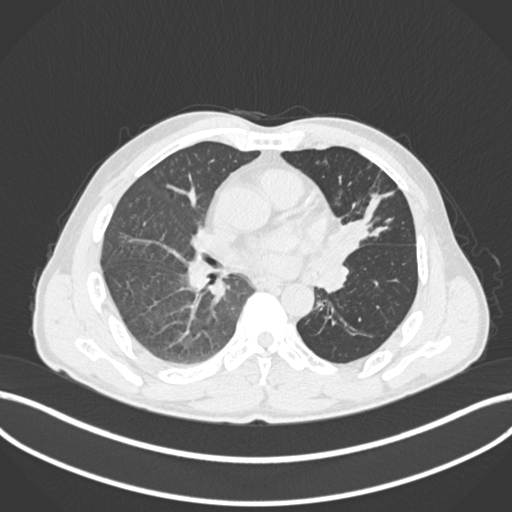
Chest CT, one axial slice; reconstruction kernel B30f; lung window (W 1500 / L -600 HU); 1 mm slice thickness; 512 × 512 image matrix. Male patient, age 57 years. From the clinical record (not read from this slice): clinical TNM (as recorded): T2b N0 M0.
Outlined on this slice (rectangle marked by the reading radiologist):
- lung tumour (recorded histology: squamous cell carcinoma): bounding box (x1, y1, x2, y2) in pixels: (320, 203, 368, 275)